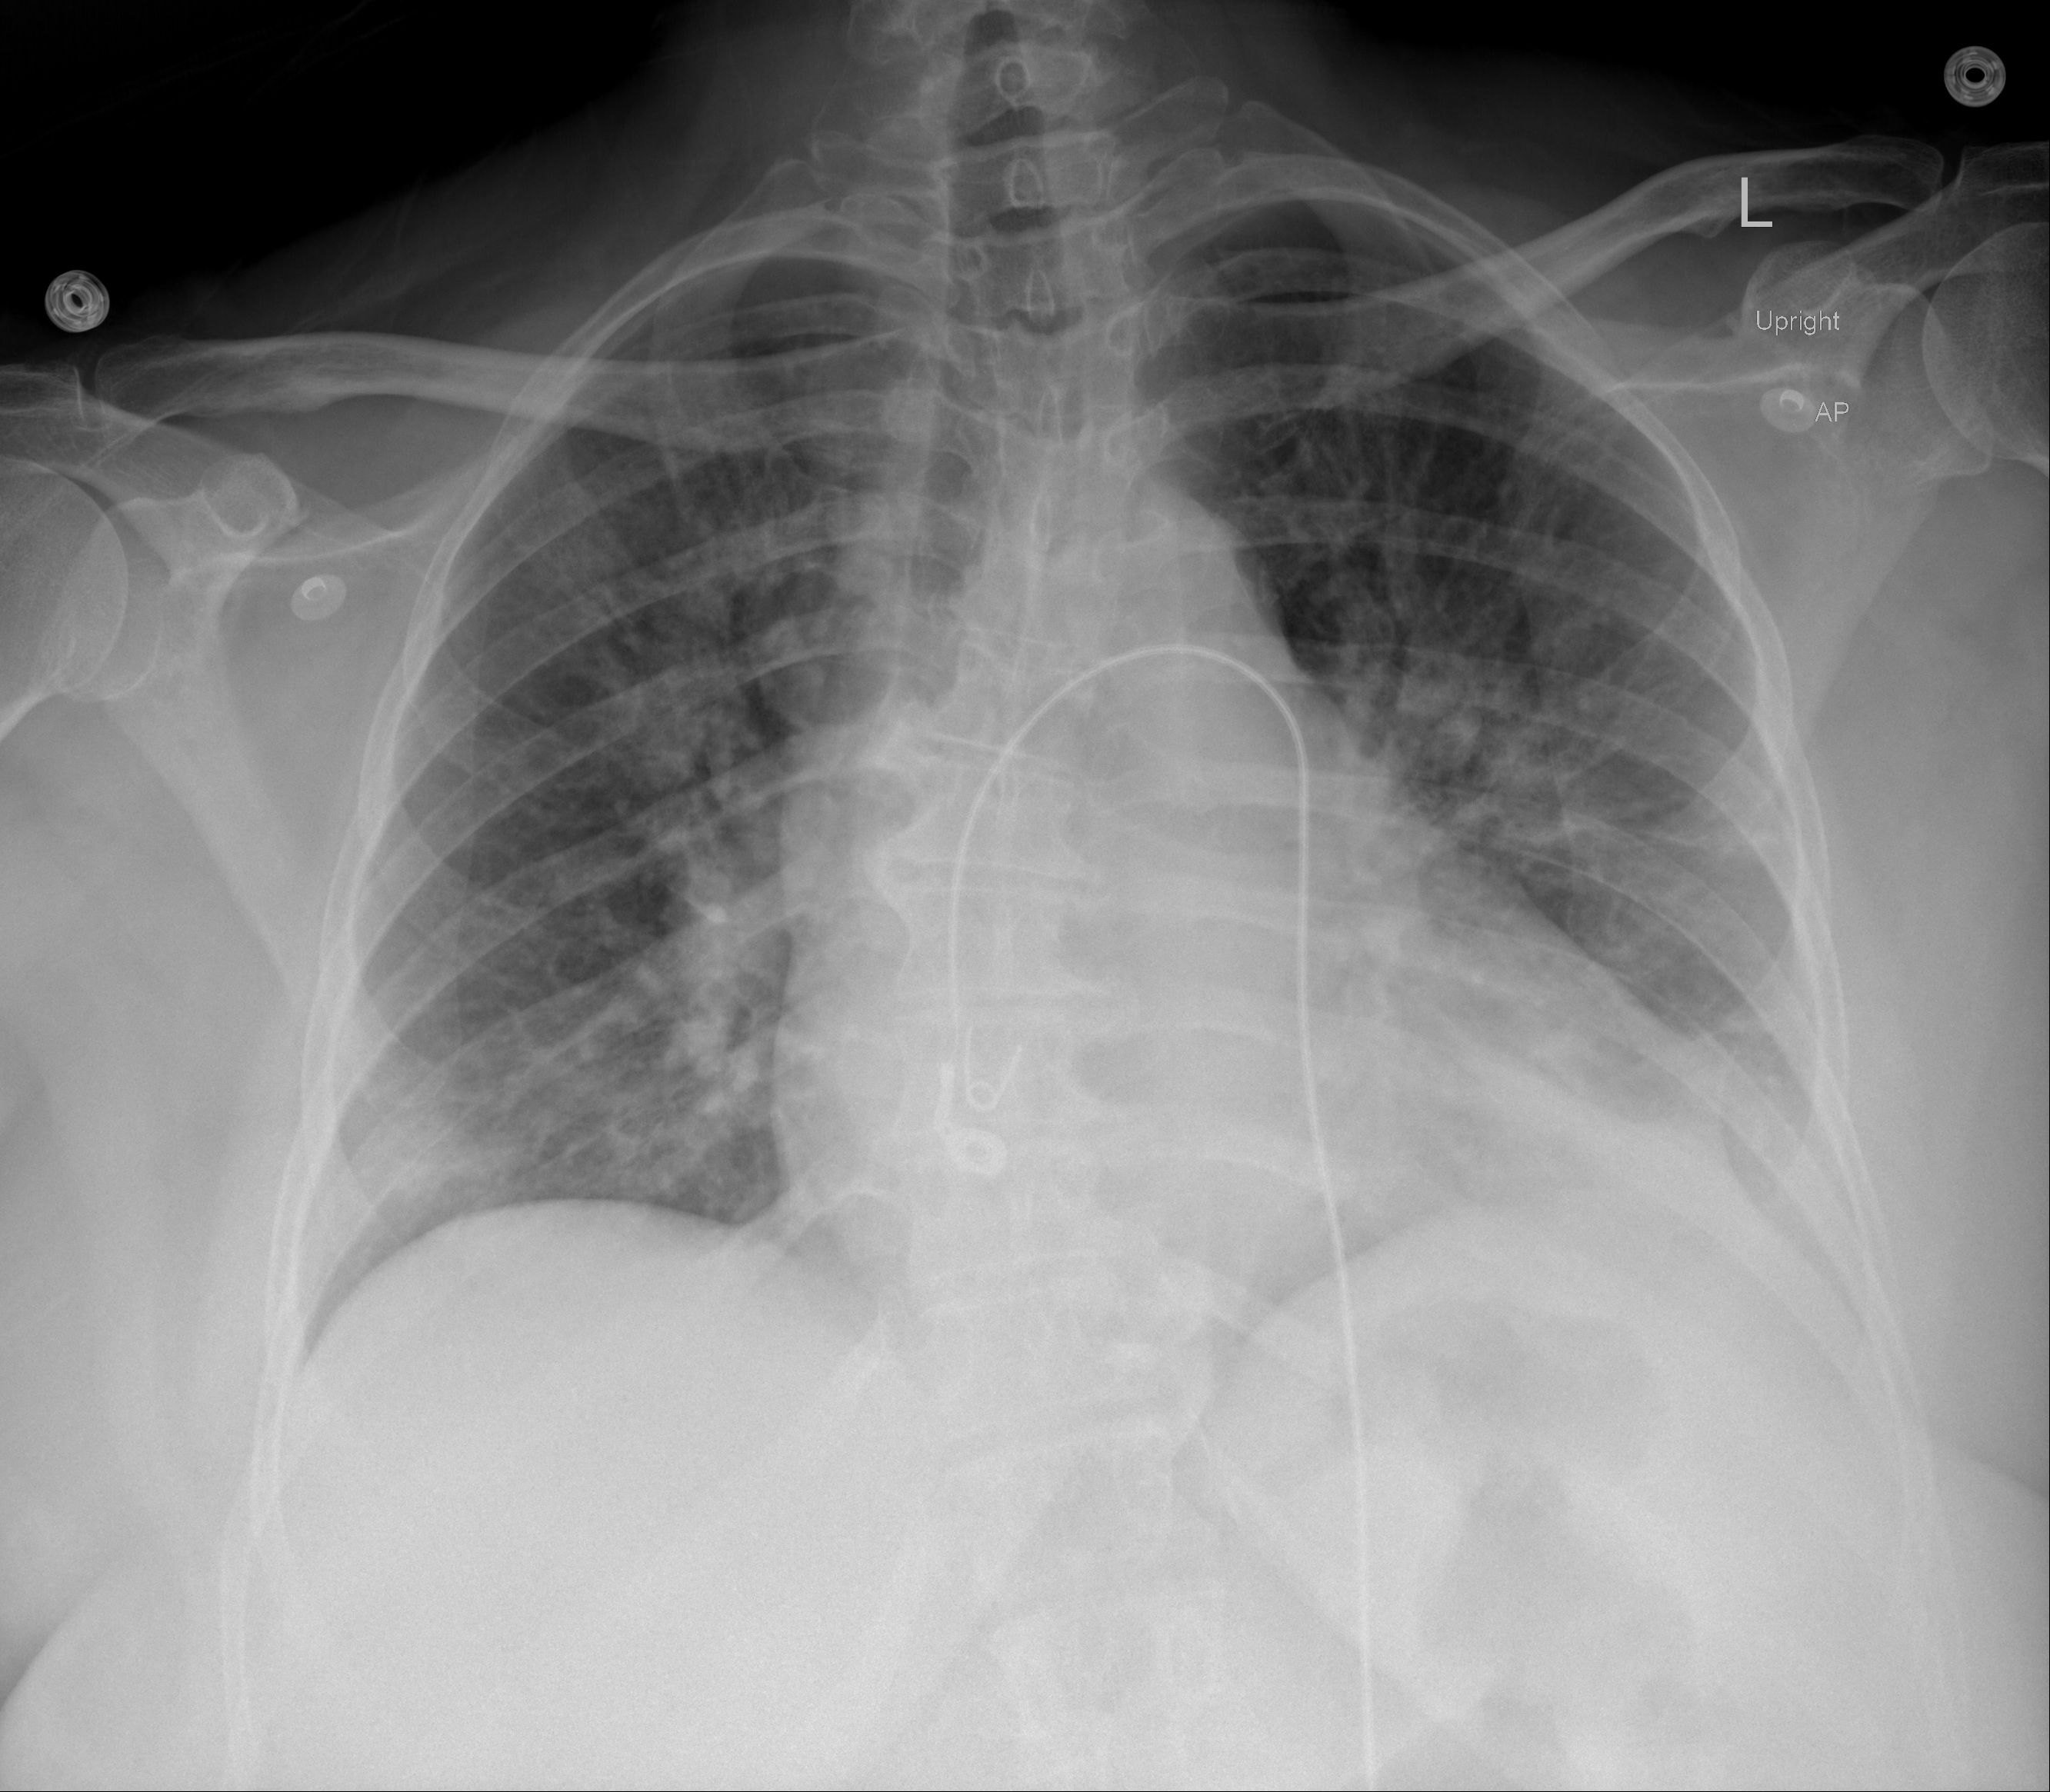
Portable chest radiograph, AP projection. Female patient, age 50 years; imaged 1 day after the COVID-19 diagnosis.
Radiologist's key findings for this exam: atelectatic and infiltrative changes more in the left retrocardiac and paracardiac region with blunting of the costophrenic sulcus.